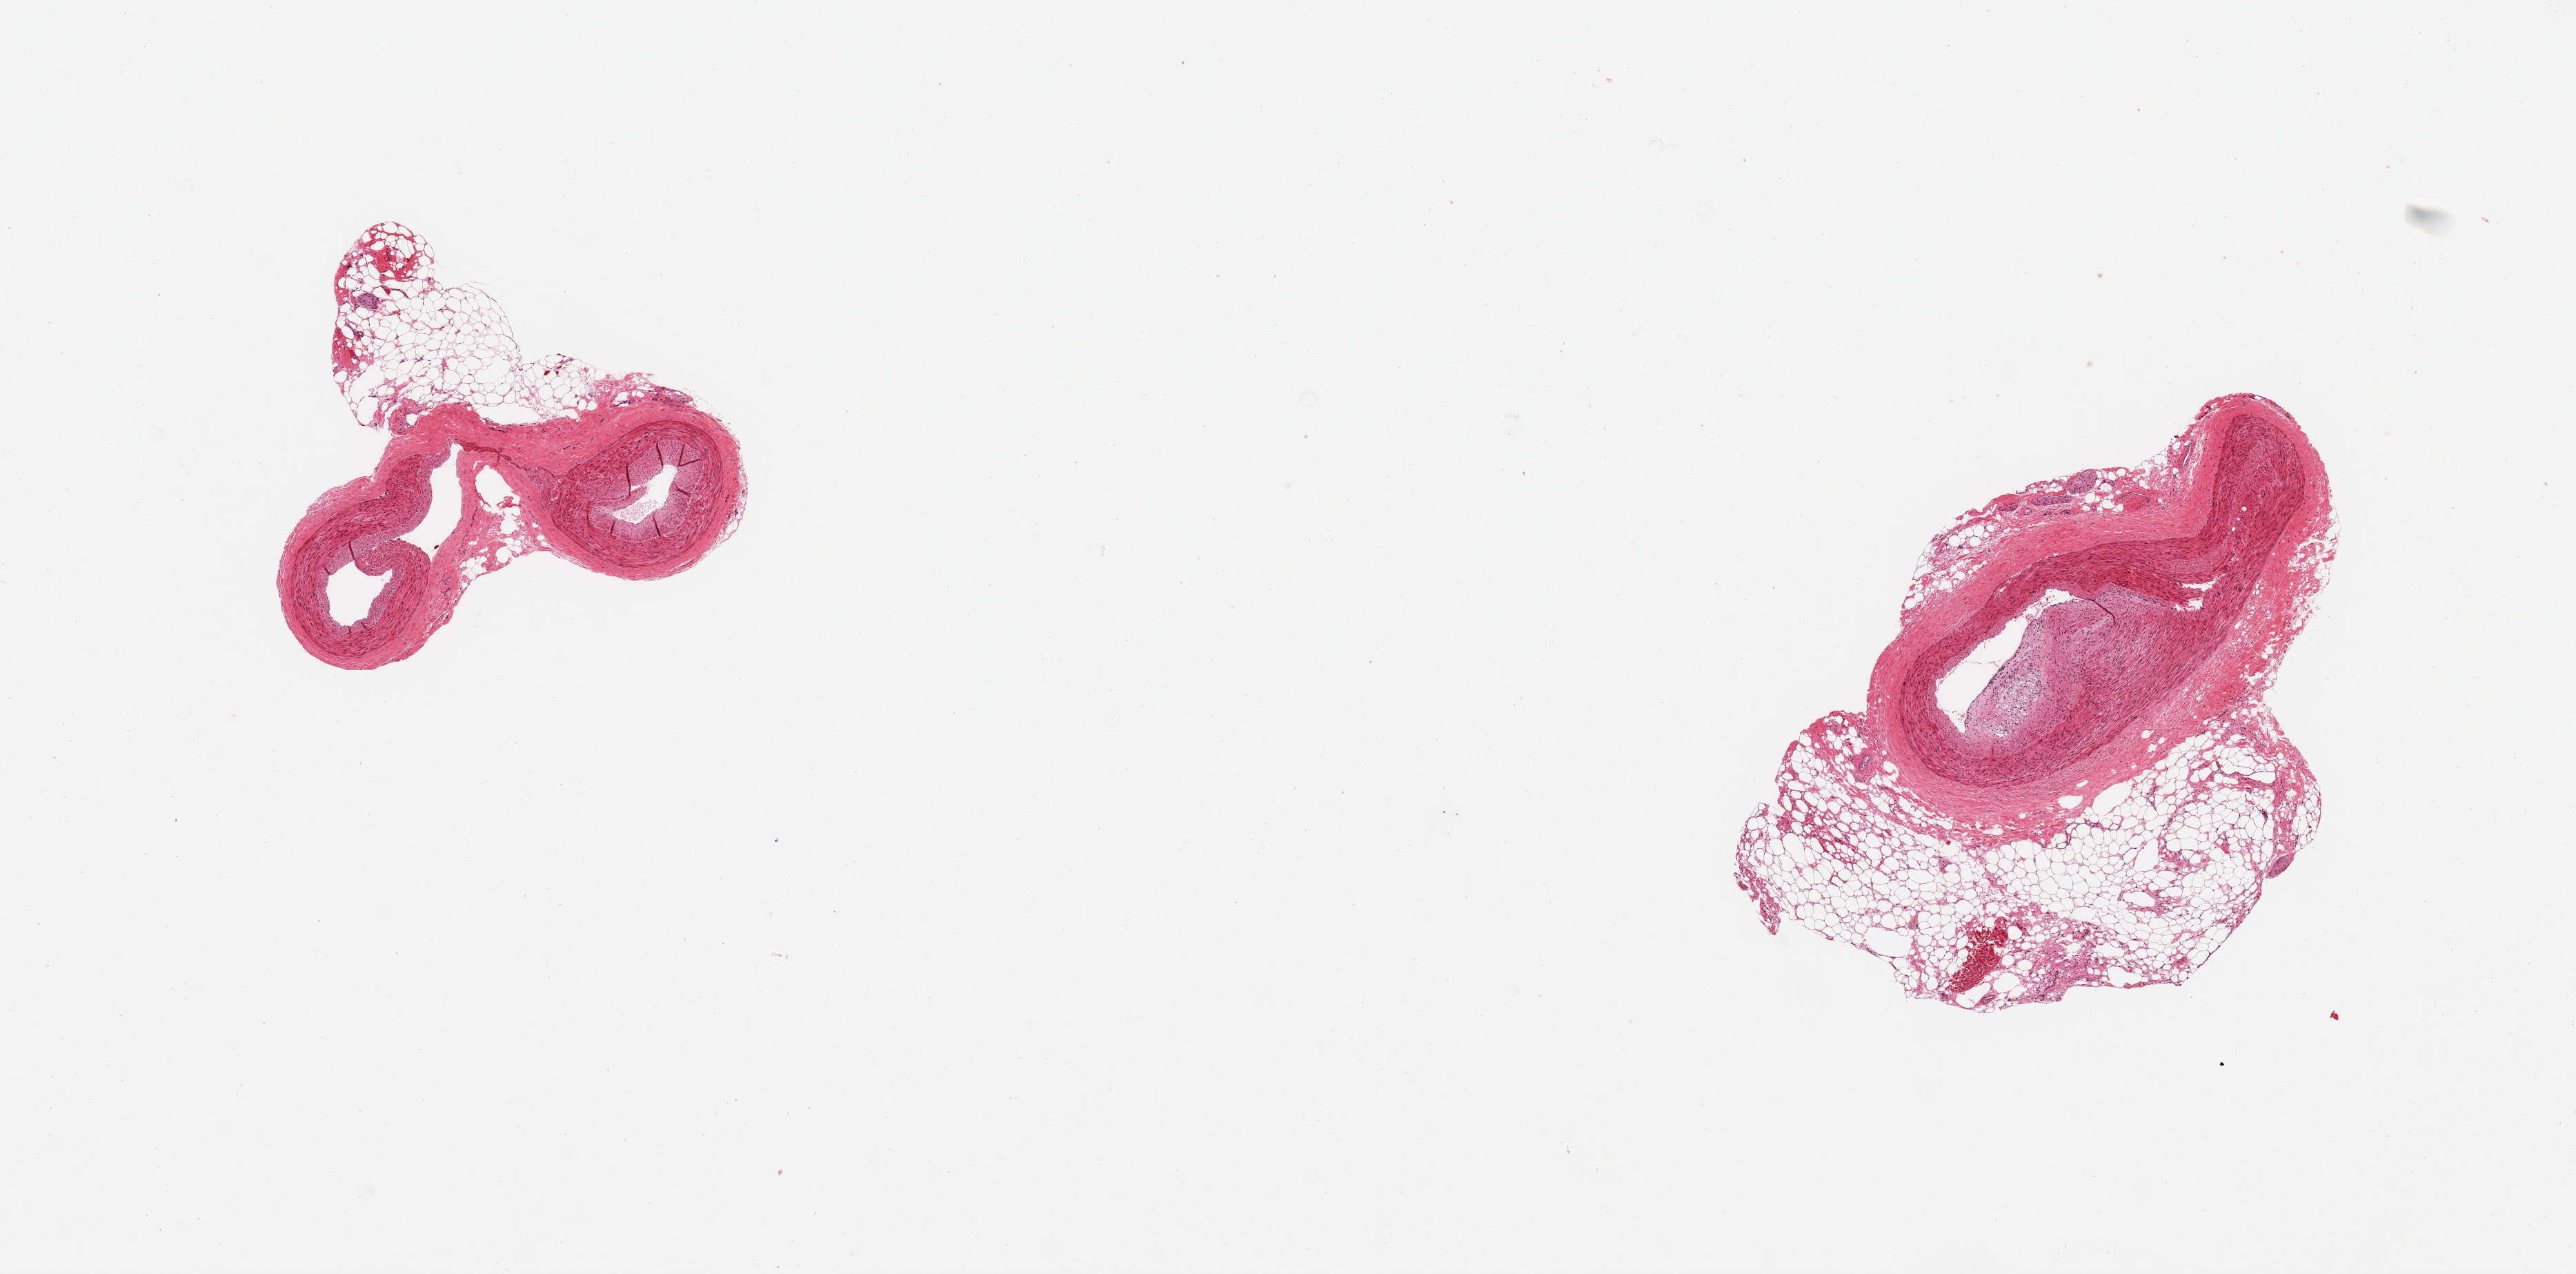
Whole-slide image, hematoxylin and eosin (H&E) stain, low-resolution overview of the scanned area, about 14.8 x 7.3 mm. PAXgene-fixed, paraffin-embedded tissue. Sampled site (target tissue): coronary artery. Donor tissue sample. Male donor.
* pathologist's review note for this sample: 2 pieces, nubbin of adherent fat up to ~1mm; focal atherosis, ~20% occlusion